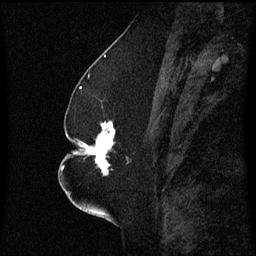
Breast MRI (dynamic contrast-enhanced), one sagittal slice. Slice 27 of 60 in the series (ordered by position). Dynamic contrast-enhanced series, image 2 of 3 at this slice position (ordered by acquisition). 1.5 T. TE 4.2 ms, TR 8.4 ms. 2.3 mm slice thickness. 256 × 256 image matrix, field of view 200 × 200 mm. Female patient, age 52 years. From the clinical record (not read from this slice): setting: breast cancer imaged before/during neoadjuvant chemotherapy; receptor status: HR-positive, HER2-negative.
Structures marked on this image (semi-automatic segmentation, software-assisted and operator-edited):
- analysis volume of interest (the breast-tissue region the enhancement analysis was run in; not a lesion): bounding box [x1, y1, x2, y2] px = [75, 122, 130, 175]
- tumour enhancement mask (voxels above the 70 % enhancement threshold inside the analysis volume of interest): [78, 122, 115, 175]